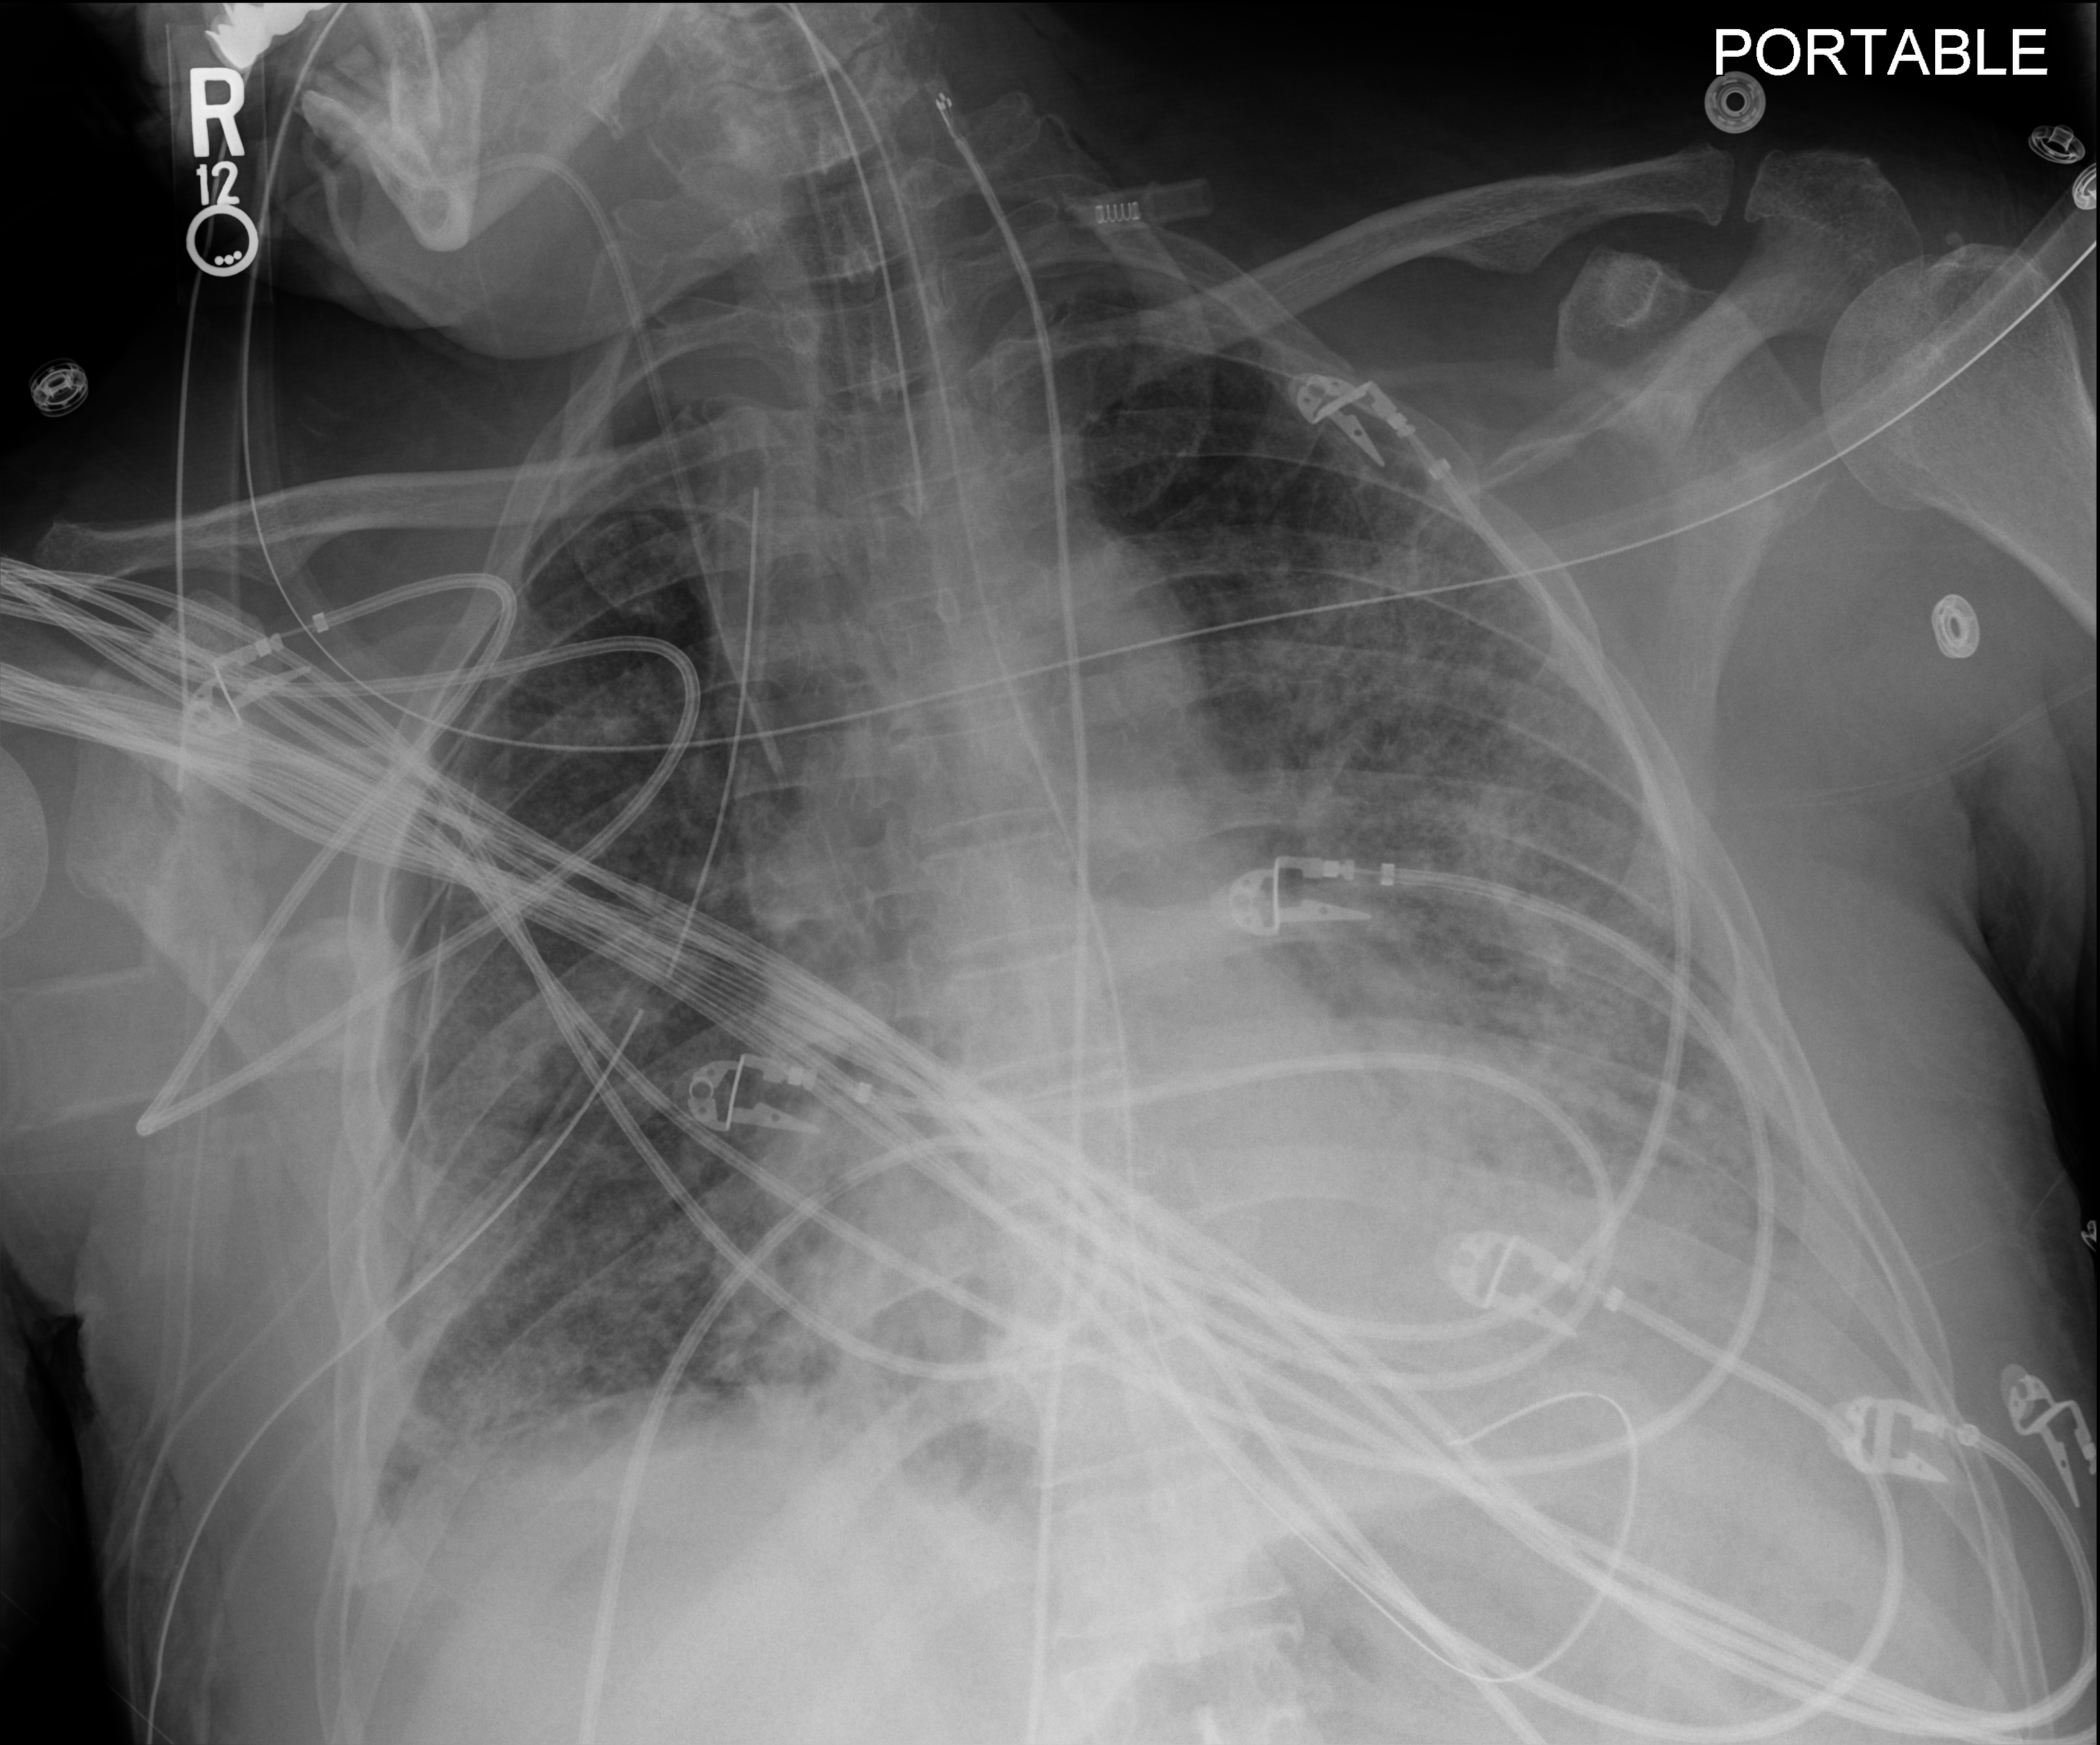
Portable chest radiograph; anteroposterior (AP) projection. Male patient hospitalised with COVID-19, age 60–74 years.
Admission-level facts for this patient (not findings on this image; timing relative to this image not recorded): hypertension (admission record): yes.